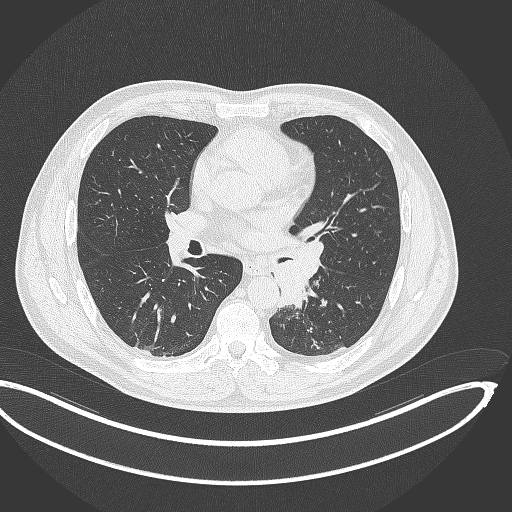
Chest CT, one axial slice; slice 186 of 362 in the series (ordered by position); reconstruction kernel B70f; lung window (W 1500 / L -600 HU); 1 mm slice thickness; 512 × 512 image matrix, field of view 442 × 442 mm. Male patient, age 50 years. From the clinical record (not read from this slice): clinical TNM (as recorded): T2a N3 M0.
Annotated regions visible in this slice (bounding box drawn by a radiologist):
- lung tumour (recorded histology: squamous cell carcinoma): box from (x=265, y=235) to (x=327, y=309) px